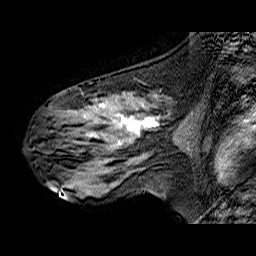
Breast MRI (dynamic contrast-enhanced), one sagittal slice; slice 35 of 60 in the series (ordered by position); dynamic contrast-enhanced series, time point 2 of 6 at this slice position (early post-contrast); 1.5 T; TE 6.3 ms, TR 32.9 ms; 4 mm slice thickness; 256 × 256 image matrix, field of view 200 × 200 mm. Female patient. From the clinical record (not read from this slice): setting: breast cancer imaged before/during neoadjuvant chemotherapy; receptor status: HER2-positive.
Structures marked on this image (semi-automatically segmented with operator editing):
- analysis volume of interest (the breast-tissue region the enhancement analysis was run in; not a lesion): bounding box [x1, y1, x2, y2] px = [34, 87, 174, 173]
- tumour enhancement mask (voxels above the 100 % enhancement threshold inside the analysis volume of interest): [94, 104, 159, 144]